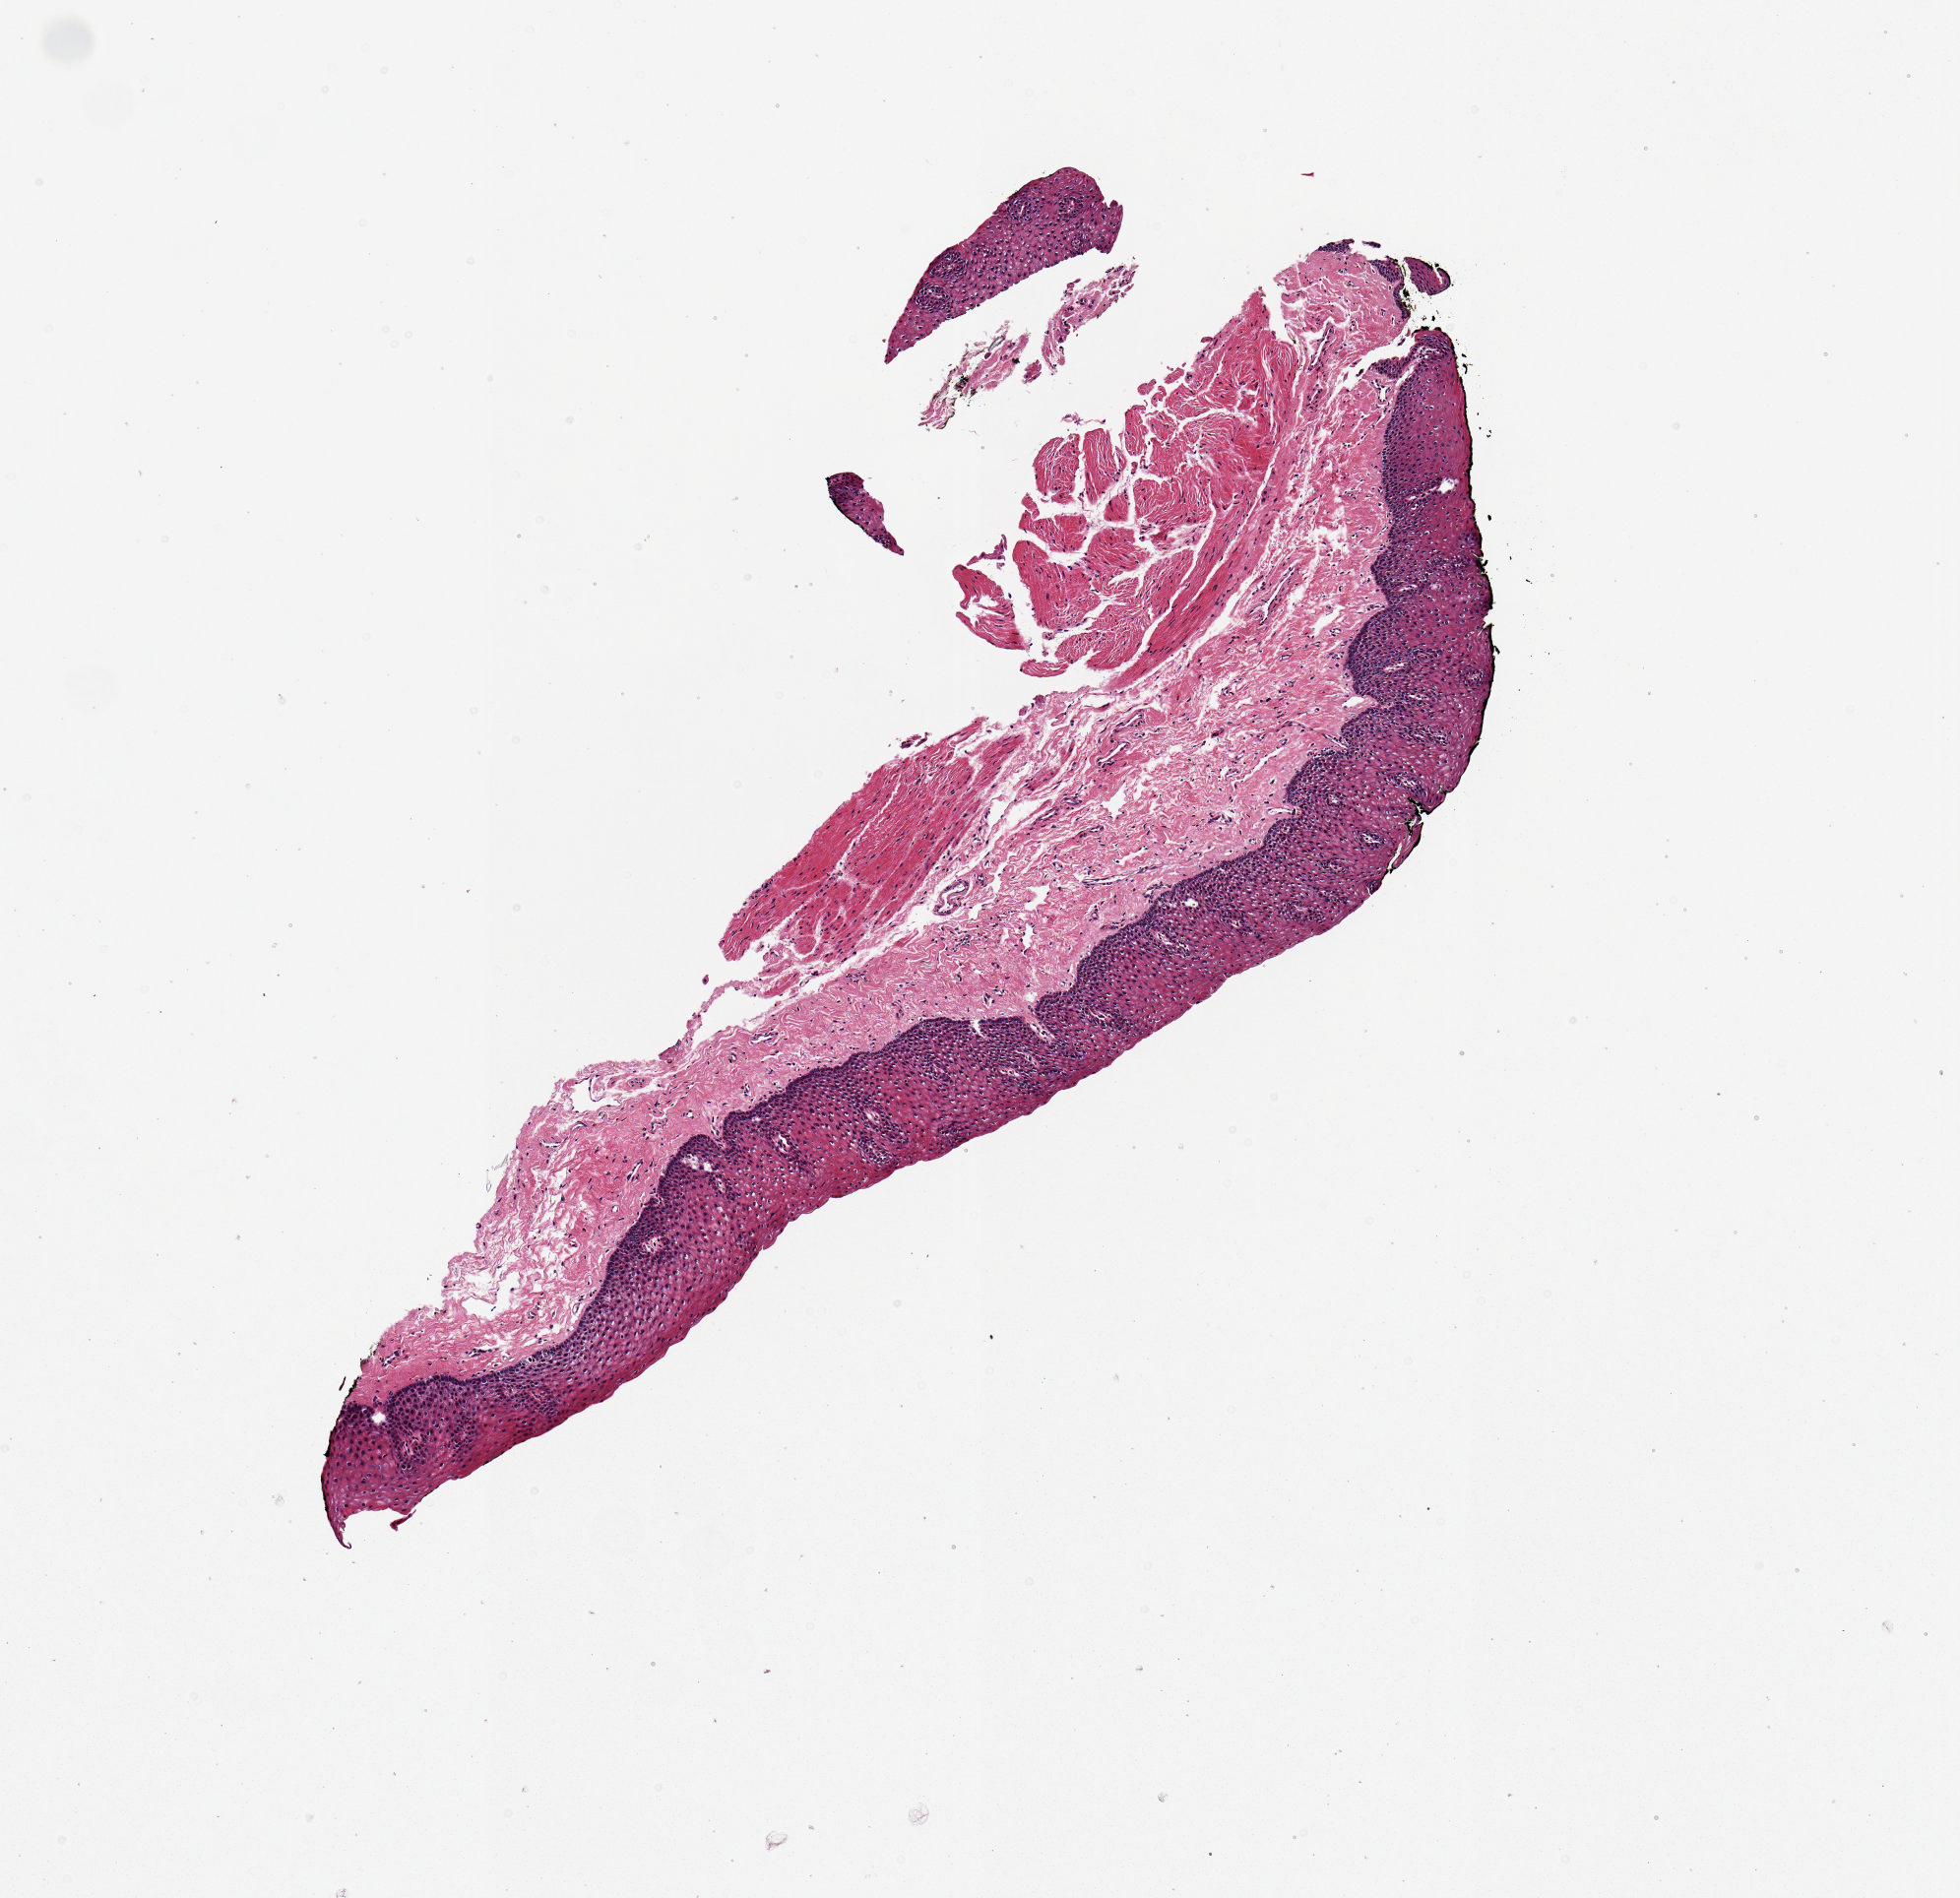
Hematoxylin and eosin (H&E) whole-slide image — shown as a low-resolution overview of the whole scanned area (about 3.9 x 3.8 mm, from a 20x scan), PAXgene-fixed, paraffin-embedded tissue, section of esophageal mucous membrane (target tissue), tissue donor sample.
* pathologist's review note for this sample: 1 piece, 3x1.5mm; squamous mucosa is ~30% thickness